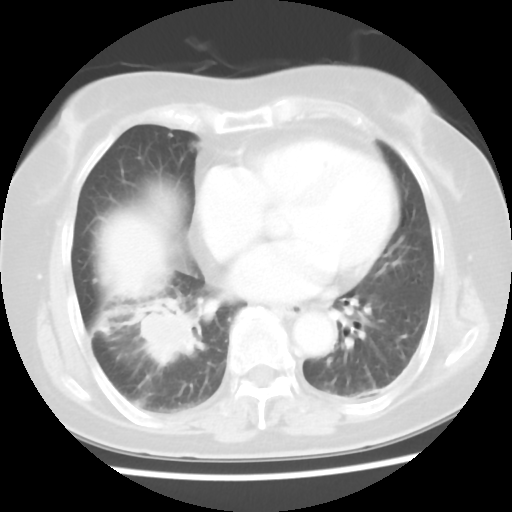
Chest CT, one axial slice; position 16 of 45 along the scan axis; lung window (W 1500 / L -600 HU); 512 × 512 image matrix, field of view 312 × 312 mm. Female patient, age 65 years. From the clinical record (not read from this slice): clinical TNM (as recorded): T2 N3 M0.
Outlined on this slice (bounding box drawn by a radiologist):
- lung tumour (recorded histology: adenocarcinoma): bounding box <125,294,198,371> (left, top, right, bottom; pixels)